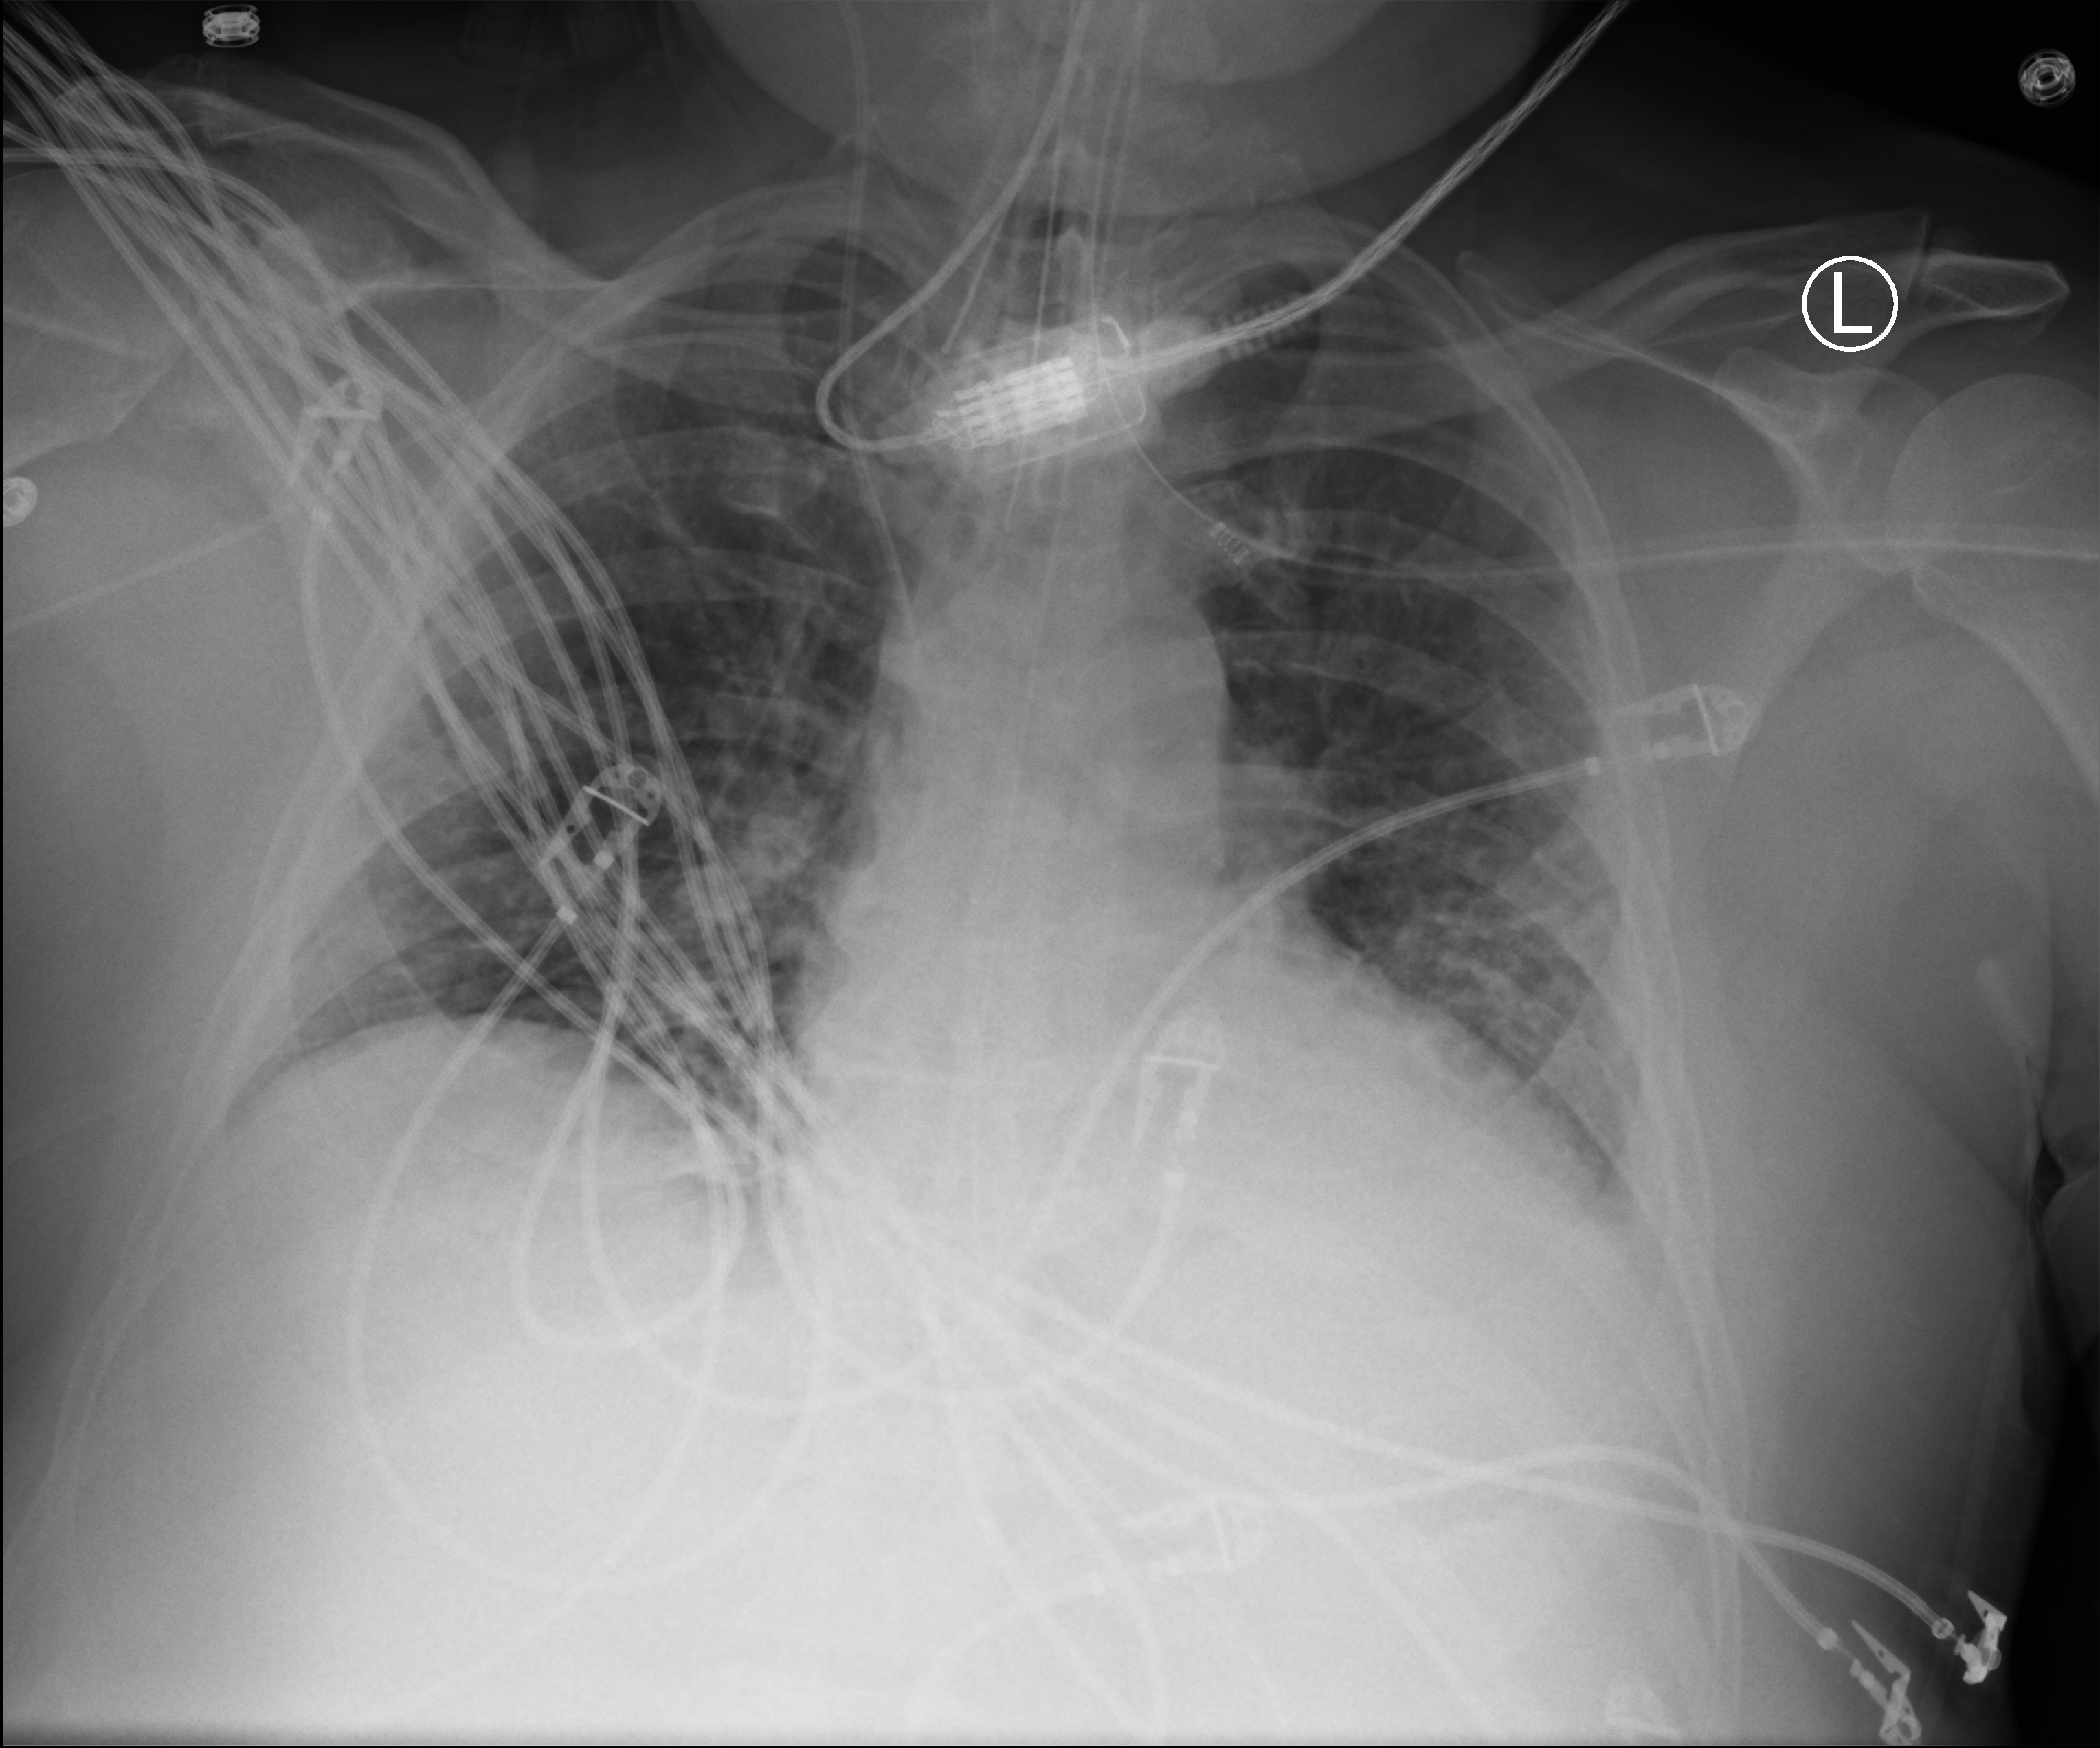
Portable chest radiograph, anteroposterior (AP) projection. Patient hospitalised with COVID-19; male, aged 18–59 years.
Admission-level facts for this patient (not findings on this image; timing relative to this image not recorded):
- mechanically ventilated during this hospital stay: yes
- COPD (admission record): no
- admitted to intensive care during this hospital stay: yes